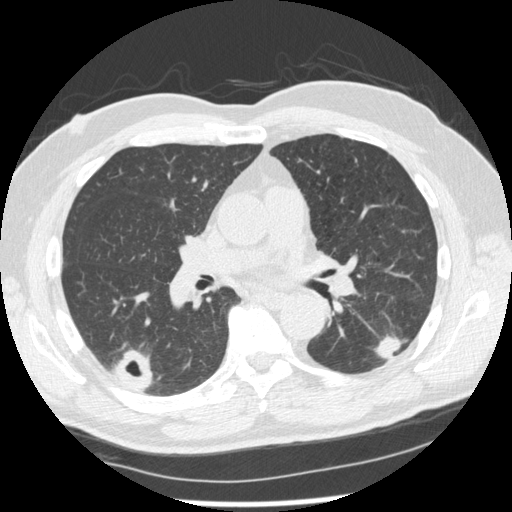
Chest CT (low-dose screening protocol), one axial image. Second screening round (one year after baseline). Lung window (W 1500 / L -600 HU). 1.25 mm slice thickness. 512 × 512 image matrix, field of view 360 × 360 mm. Male, age 74 years at enrolment. Former smoker at enrolment.
Lesion marked by an expert reader, box from (x=370, y=315) to (x=422, y=368) px. The screening reader recorded 7 non-calcified nodules or masses ≥4 mm on this exam (right upper lobe, right lower lobe, right upper lobe, right lower lobe, left lower lobe, left upper lobe, left upper lobe); which of them this box marks is not recorded. Official screen result: positive, other. Later outcome: lung cancer diagnosed 43 days after this screen — squamous cell carcinoma, NOS, left lower lobe, well differentiated (G1), stage IA (AJCC 6th edition), 28 mm at pathology.